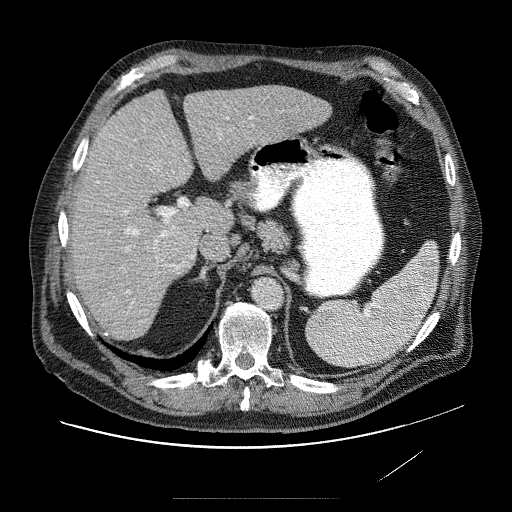
Contrast-enhanced abdominal CT (liver protocol), one axial slice; slice 49 of 89 in the series (ordered by position); 120 kVp; soft-tissue window (W 400 / L 40 HU); 2.5 mm slice thickness; 512 × 512 image matrix. From the clinical record (not read from this slice): diagnosis: hepatocellular carcinoma (patient treated with transarterial chemoembolisation; whether this scan precedes or follows treatment is not stated here); TNM stage (as recorded): Stage-IVA; Child-Pugh class: A; tumour differentiation: moderately differentiated; tumour nodularity: multinodular.
Structures marked on this image (semi-automatically segmented with operator editing):
- abdominal aorta: bounding box <252,278,282,308> (left, top, right, bottom; pixels)
- liver parenchyma outside the tumour (the mass and vessels are separate outlines, so this box may not span the whole liver): <66,84,334,334>
- mass: <148,137,191,262>
- liver vessels: <96,118,293,312>